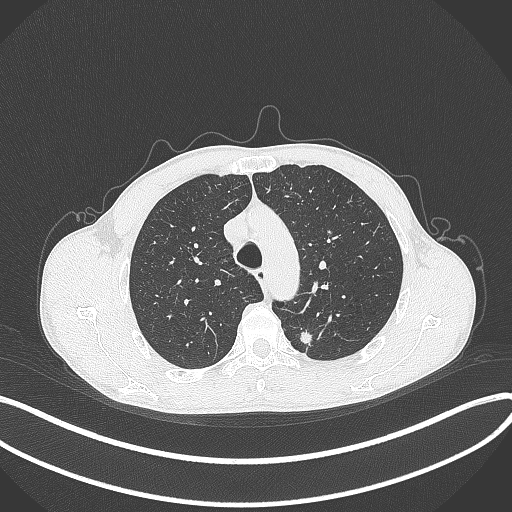
Chest CT, one axial slice; position 302 of 429 along the scan axis; reconstruction kernel B70f; lung window (W 1500 / L -600 HU); 512 × 512 image matrix. Male patient, age 51 years. Case-level facts recorded for this patient, not image findings: clinical TNM (as recorded): T2a N1 M1.
Annotated regions visible in this slice (bounding box drawn by a radiologist):
- lung tumour (recorded histology: adenocarcinoma): bounding box (x1, y1, x2, y2) in pixels: (294, 325, 317, 350)